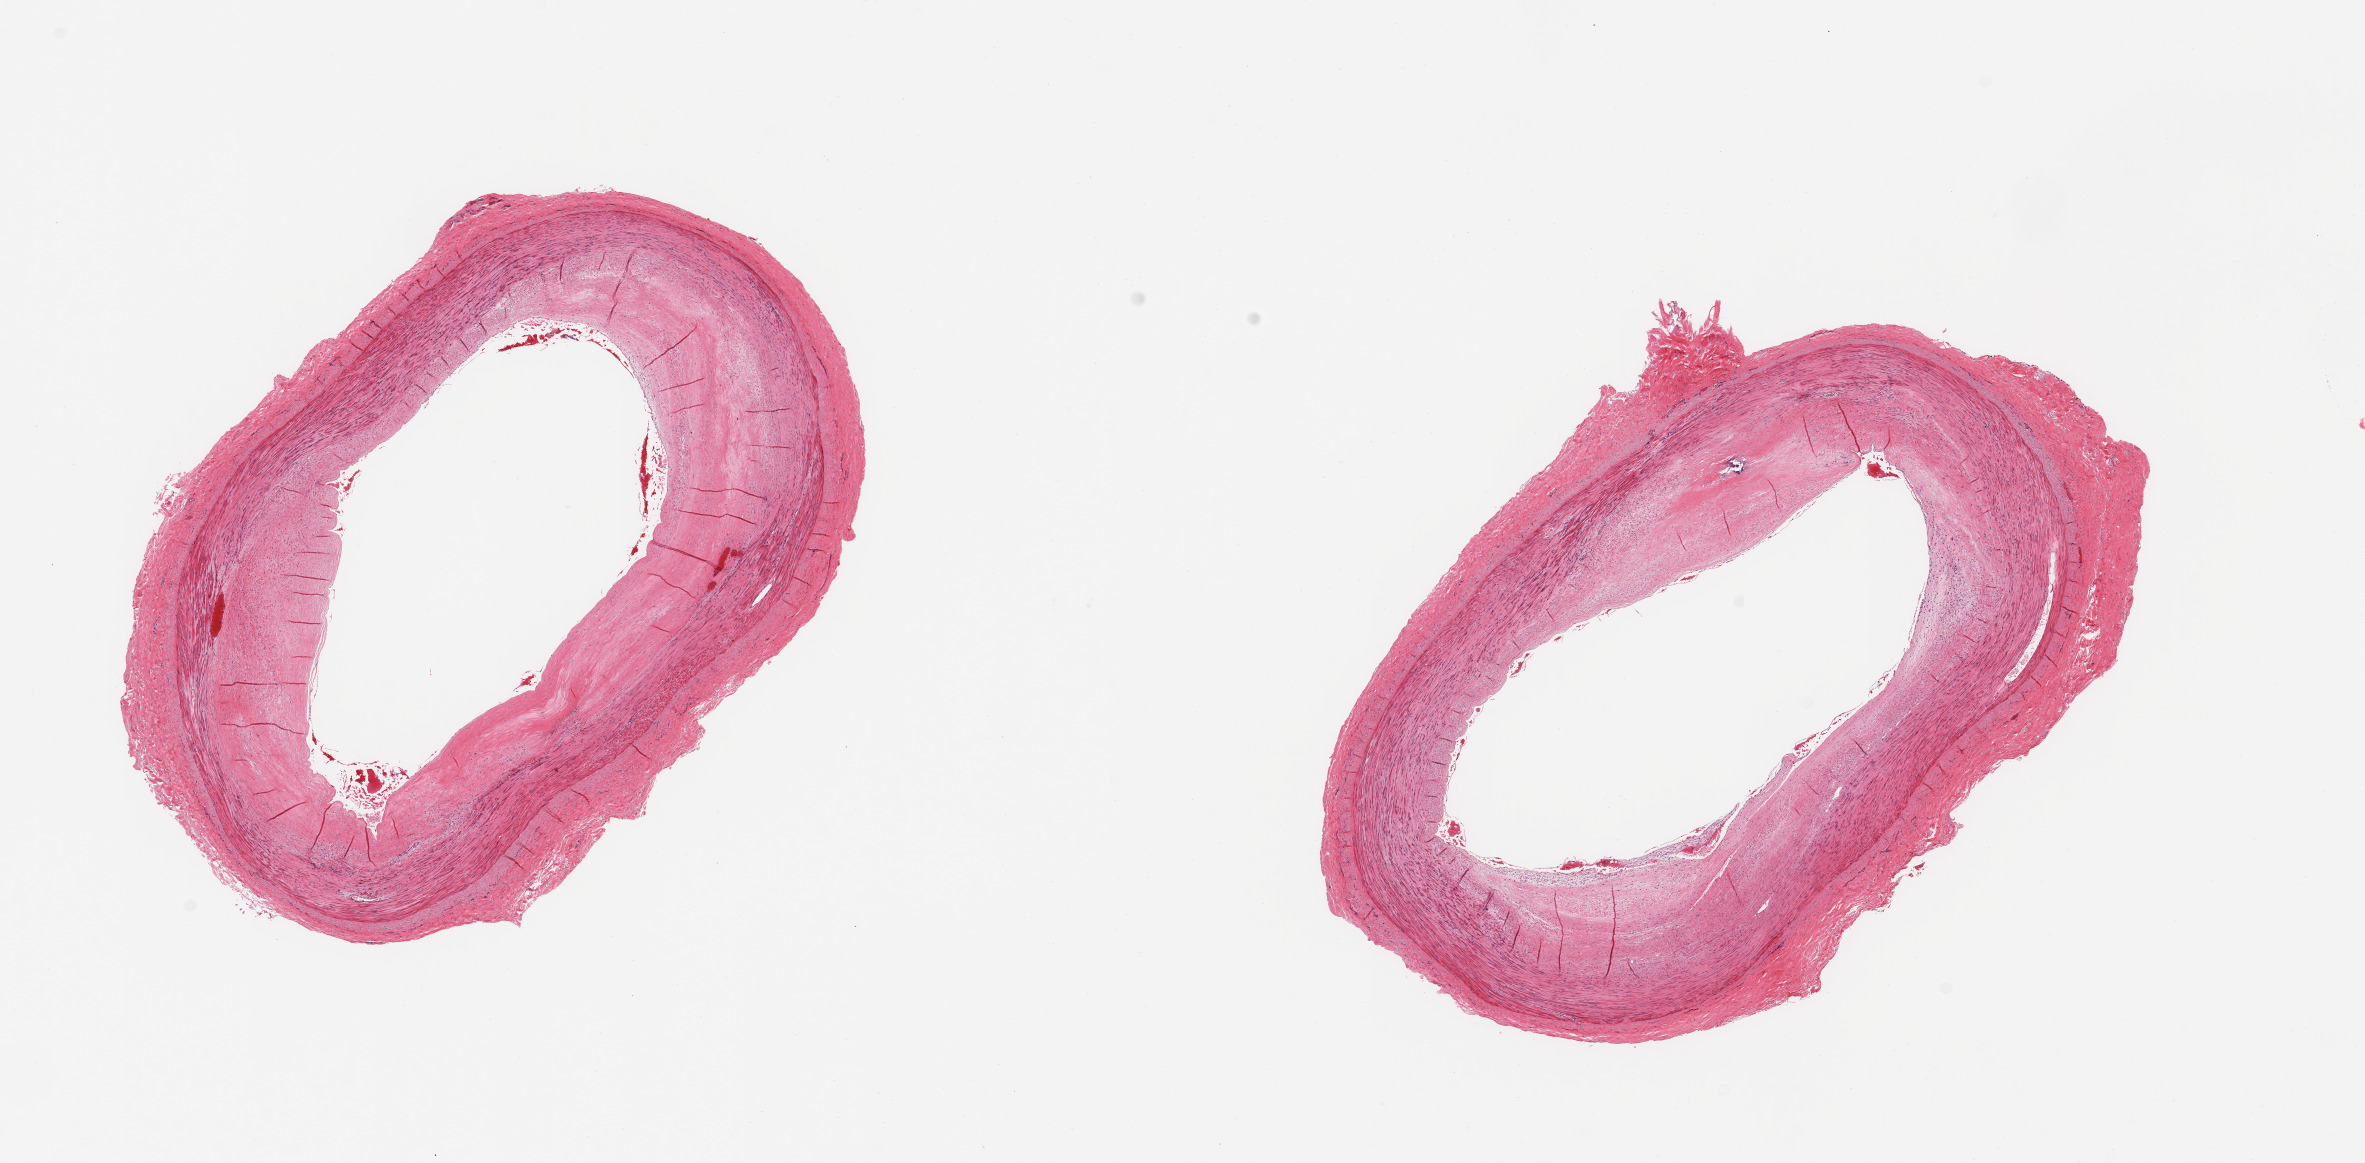
Whole-slide image, haematoxylin and eosin stain — low-resolution overview of the scanned area, about 18.7 x 9.2 mm; PAXgene-fixed, paraffin-embedded tissue; section of tibial artery (target tissue); tissue donor sample. Donor sex: male.
* pathologist's review note for this sample: 2 pieces, minimal adherant fat; ~50% occlusive atheriosis, focally calcified